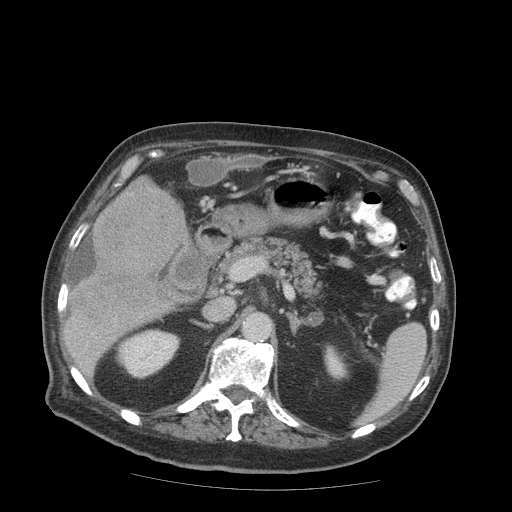
Contrast-enhanced abdominal CT (liver protocol), one axial slice. Position 40 of 99 along the scan axis. Reconstruction kernel STANDARD. 140 kVp. Soft-tissue window (W 400 / L 40 HU). 2.5 mm slice thickness. 512 × 512 image matrix. Case-level facts recorded for this patient, not image findings: diagnosis: hepatocellular carcinoma (patient treated with transarterial chemoembolisation; whether this scan precedes or follows treatment is not stated here); TNM stage (as recorded): Stage-IIIB; Child-Pugh class: A; tumour nodularity: multinodular.
Annotated regions visible in this slice (semi-automatically segmented with operator editing):
- liver parenchyma outside the tumour (the mass and vessels are separate outlines, so this box may not span the whole liver): bounding box (x1, y1, x2, y2) in pixels: (70, 180, 190, 340)
- mass: (69, 177, 186, 328)